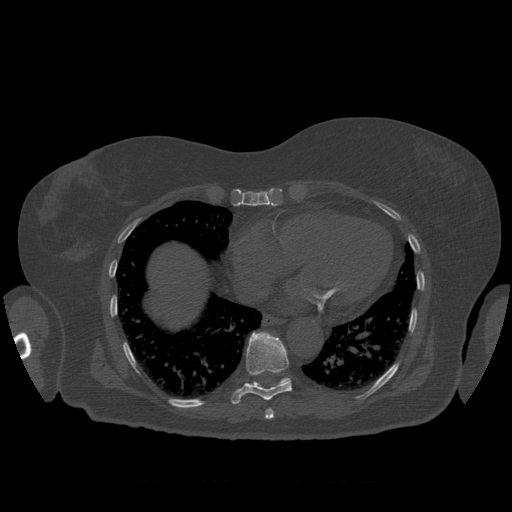
CT including the spine, one axial slice. Slice 357 of 399 in the series (ordered by position). Reconstruction kernel STANDARD. 120 kVp. Bone window (W 1800 / L 400 HU). 512 × 512 image matrix, field of view 404 × 404 mm. Patient age 81 years. Case-level facts recorded for this patient, not image findings: primary cancer: renal; vertebrae with lytic lesions (as recorded): L1.
Annotated regions visible in this slice (semi-automatically segmented with operator editing):
- T10 vertebra: bounding box <249,378,291,387> (left, top, right, bottom; pixels)
- T8 vertebra: <265,409,274,420>
- T9 vertebra: <231,332,293,404>